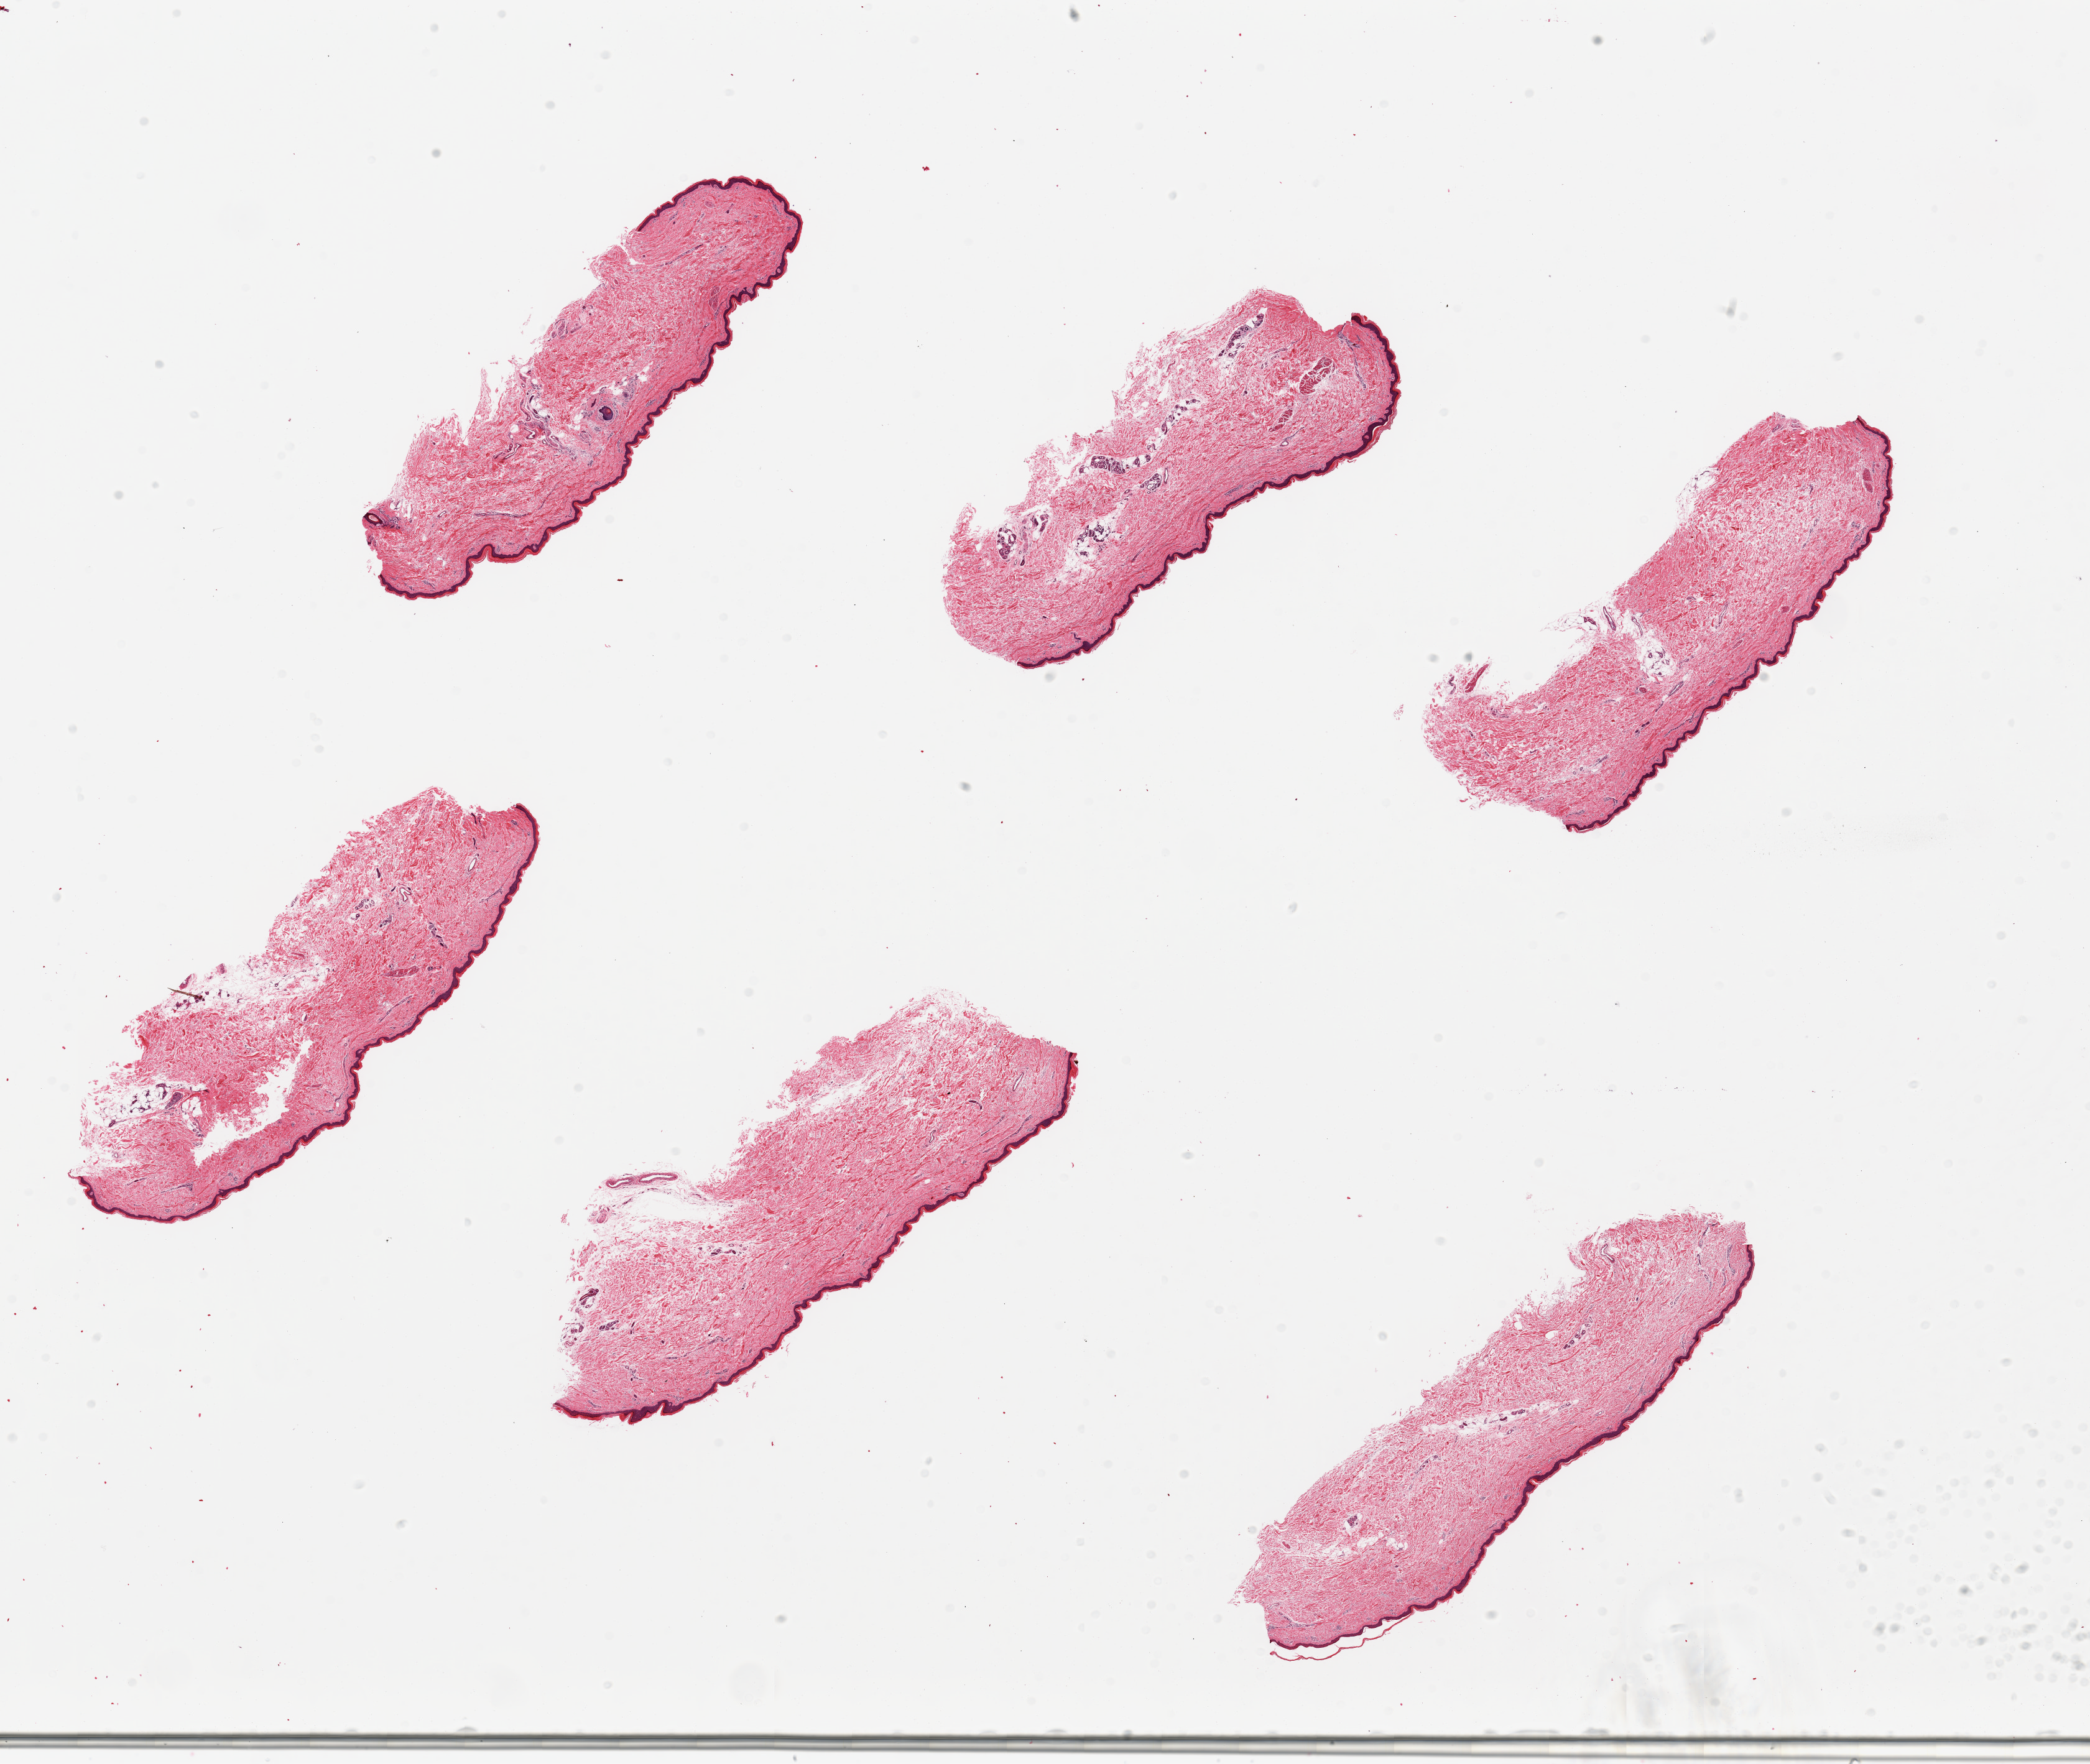
Hematoxylin and eosin (H&E) whole-slide image, whole scanned area (about 26.6 x 22.4 mm, from a 20x scan) shown as a low-resolution overview, PAXgene-fixed, paraffin-embedded tissue, target tissue: skin of lower leg, donor tissue sample. Donor sex: female.
Pathologist's review note for this sample: 6 pieces, well trimmed, squamous epithelium measures ~50 microns.